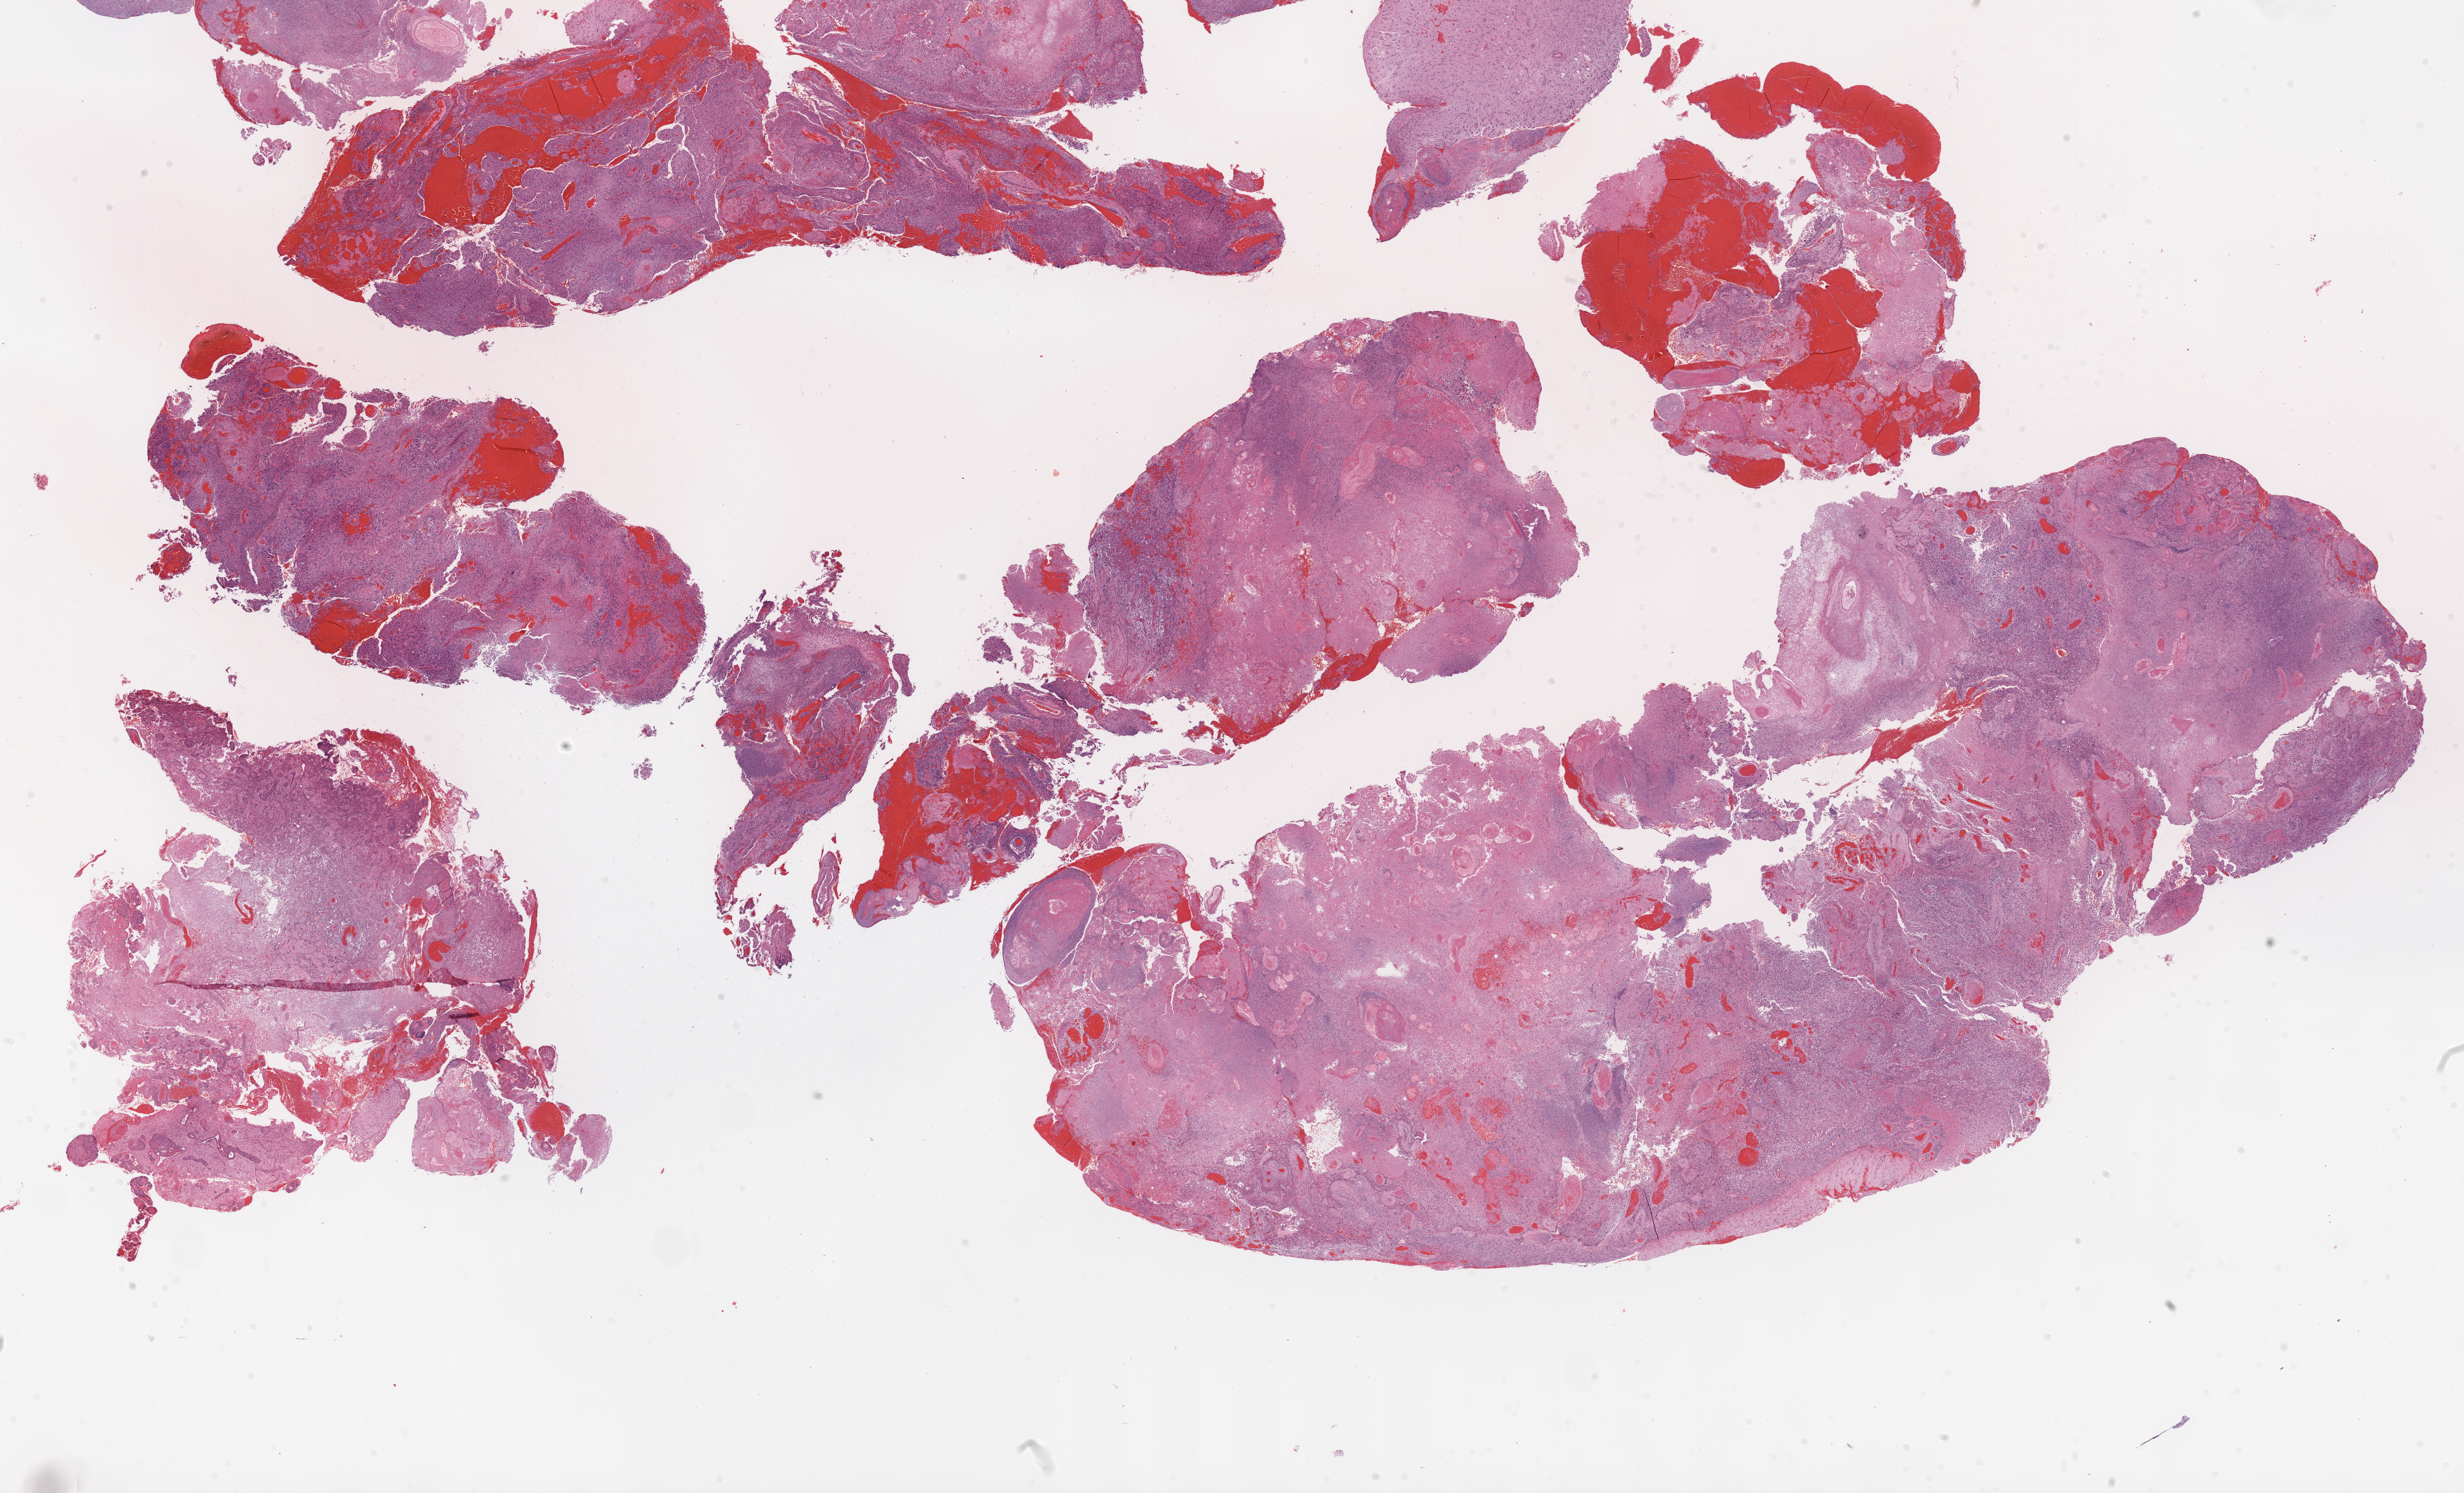
Digitized H&E tissue section (whole slide), whole scanned area (about 32.1 x 19.5 mm, acquisition: 20x scan) shown as a low-resolution overview; FFPE section; brain, primary tumour sample. Male, age 55 years at initial diagnosis.
Diagnosis: Glioblastoma.